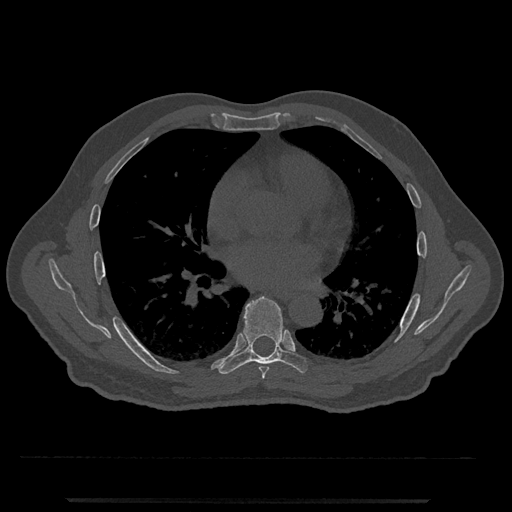
CT including the spine, one axial slice. Position 698 of 797 along the scan axis. Reconstruction kernel Br40s/3. 120 kVp. Bone window (W 1800 / L 400 HU). 0.5 mm slice thickness. 512 × 512 image matrix, field of view 419 × 419 mm. Male patient, age 63 years. From the clinical record (not read from this slice): primary cancer: prostate.
Structures marked on this image (semi-automatic segmentation, software-assisted and operator-edited):
- T6 vertebra: bounding box (x1, y1, x2, y2) in pixels: (259, 366, 269, 379)
- T7 vertebra: (217, 296, 308, 375)